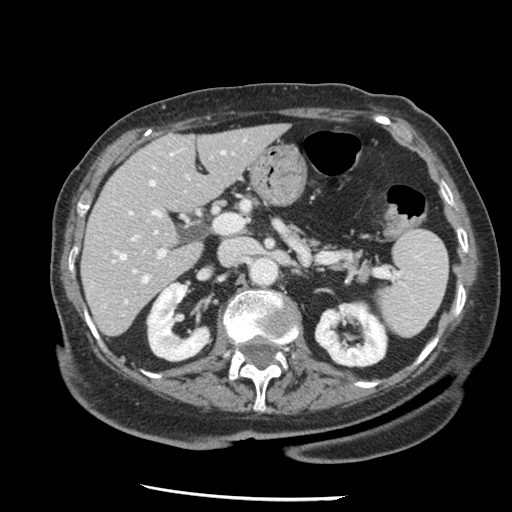
Contrast-enhanced abdominal CT, one axial slice; slice 73 of 148 in the series (ordered by position); reconstruction kernel STANDARD; 120 kVp; intravenous contrast given; soft-tissue window (W 400 / L 40 HU); 2.5 mm slice thickness; 512 × 512 image matrix. Female patient, age 85 years. Case-level facts recorded for this patient, not image findings: diagnosis: colorectal cancer liver metastases, imaged before liver resection; multiple liver metastases: no; largest metastasis: 0.9 cm.
Annotated regions visible in this slice (outlined manually by an expert reader):
- hepatic veins: box from (x=115, y=148) to (x=184, y=303) px
- liver: (x=83, y=126)–(x=285, y=336)
- planned liver remnant (the part of the liver to remain after resection): (x=83, y=126)–(x=285, y=336)
- portal vein (with intrahepatic branches): (x=129, y=149)–(x=227, y=273)